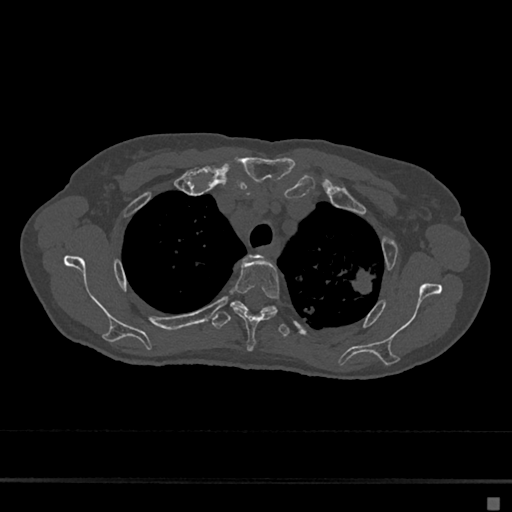
CT including the spine, one axial slice; slice 530 of 797 in the series (ordered by position); reconstruction kernel Br40s/3; 120 kVp; bone window (W 1800 / L 400 HU); 512 × 512 image matrix. Patient: female, 68 years. From the clinical record (not read from this slice): primary cancer: renal.
Outlined on this slice (semi-automatic segmentation, software-assisted and operator-edited):
- T2 vertebra: bounding box (x1, y1, x2, y2) in pixels: (233, 255, 262, 307)
- T3 vertebra: (232, 259, 280, 351)
- T4 vertebra: (211, 301, 290, 337)